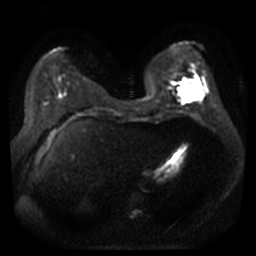
Breast MRI, one axial slice; slice 12 of 44 in the series (ordered by position); diffusion-weighted series; image 2 of 4 stored at this slice position (different b-values; order by instance number); 3 T; 5 mm slice thickness; 256 × 256 image matrix, field of view 360 × 360 mm. Female patient.
Annotated regions visible in this slice (outlined manually by an expert reader):
- tumour on diffusion-weighted imaging: bounding box <178,82,204,103> (left, top, right, bottom; pixels)